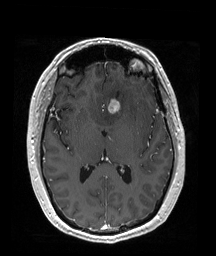
Brain MRI from a brain-tumour surgery series, one axial slice; slice 95 of 192 in the series (ordered by position); T1-weighted post-contrast; 1 mm slice thickness; 216 × 256 image matrix, field of view 211 × 250 mm. From the clinical record (not read from this slice): histopathology: Oligodendroglioma; WHO grade: 2; IDH mutation: yes; tumour location: Left Frontal (septal).
Outlined on this slice (outlined manually by an expert reader):
- tumour: bounding box (x1, y1, x2, y2) in pixels: (114, 98, 127, 113)